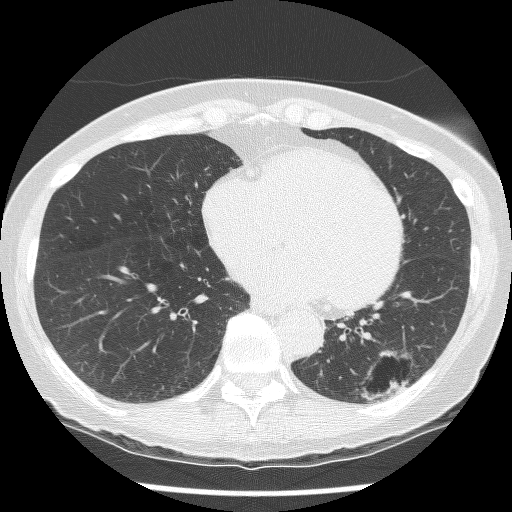
Low-dose screening chest CT, axial slice, second annual screen, lung window (W 1500 / L -600 HU), 512 × 512 image matrix, field of view 300 × 300 mm. Female participant, aged 61 years at enrolment.
Expert-annotated lung lesion, box from (x=334, y=333) to (x=435, y=418) px. The screening reader recorded 2 non-calcified nodules or masses ≥4 mm on this exam (left lower lobe, left lower lobe); which of them this box marks is not recorded. Participant outcome: lung cancer diagnosed 585 days after this screen — non-small cell carcinoma, left lower lobe, poorly differentiated (G3), stage IB (AJCC 6th edition), 100 mm at pathology.